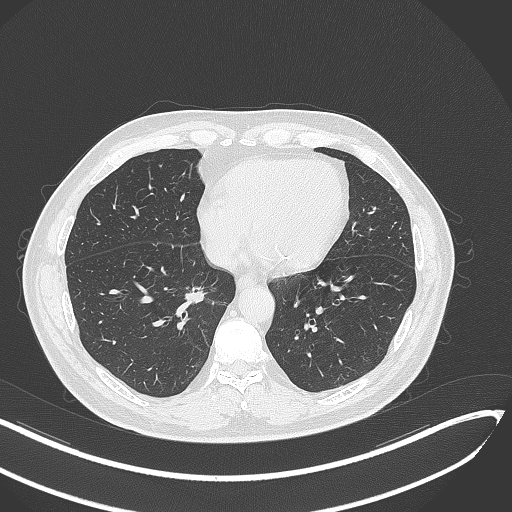
Chest CT, one axial slice; position 134 of 429 along the scan axis; 120 kVp; lung window (W 1500 / L -600 HU); 1 mm slice thickness; 512 × 512 image matrix, field of view 400 × 400 mm. Male patient, age 62 years. From the clinical record (not read from this slice): clinical TNM (as recorded): T1b N0 M0.
Structures marked on this image (rectangle marked by the reading radiologist):
- lung tumour (recorded histology: adenocarcinoma): box from (x=185, y=285) to (x=211, y=306) px